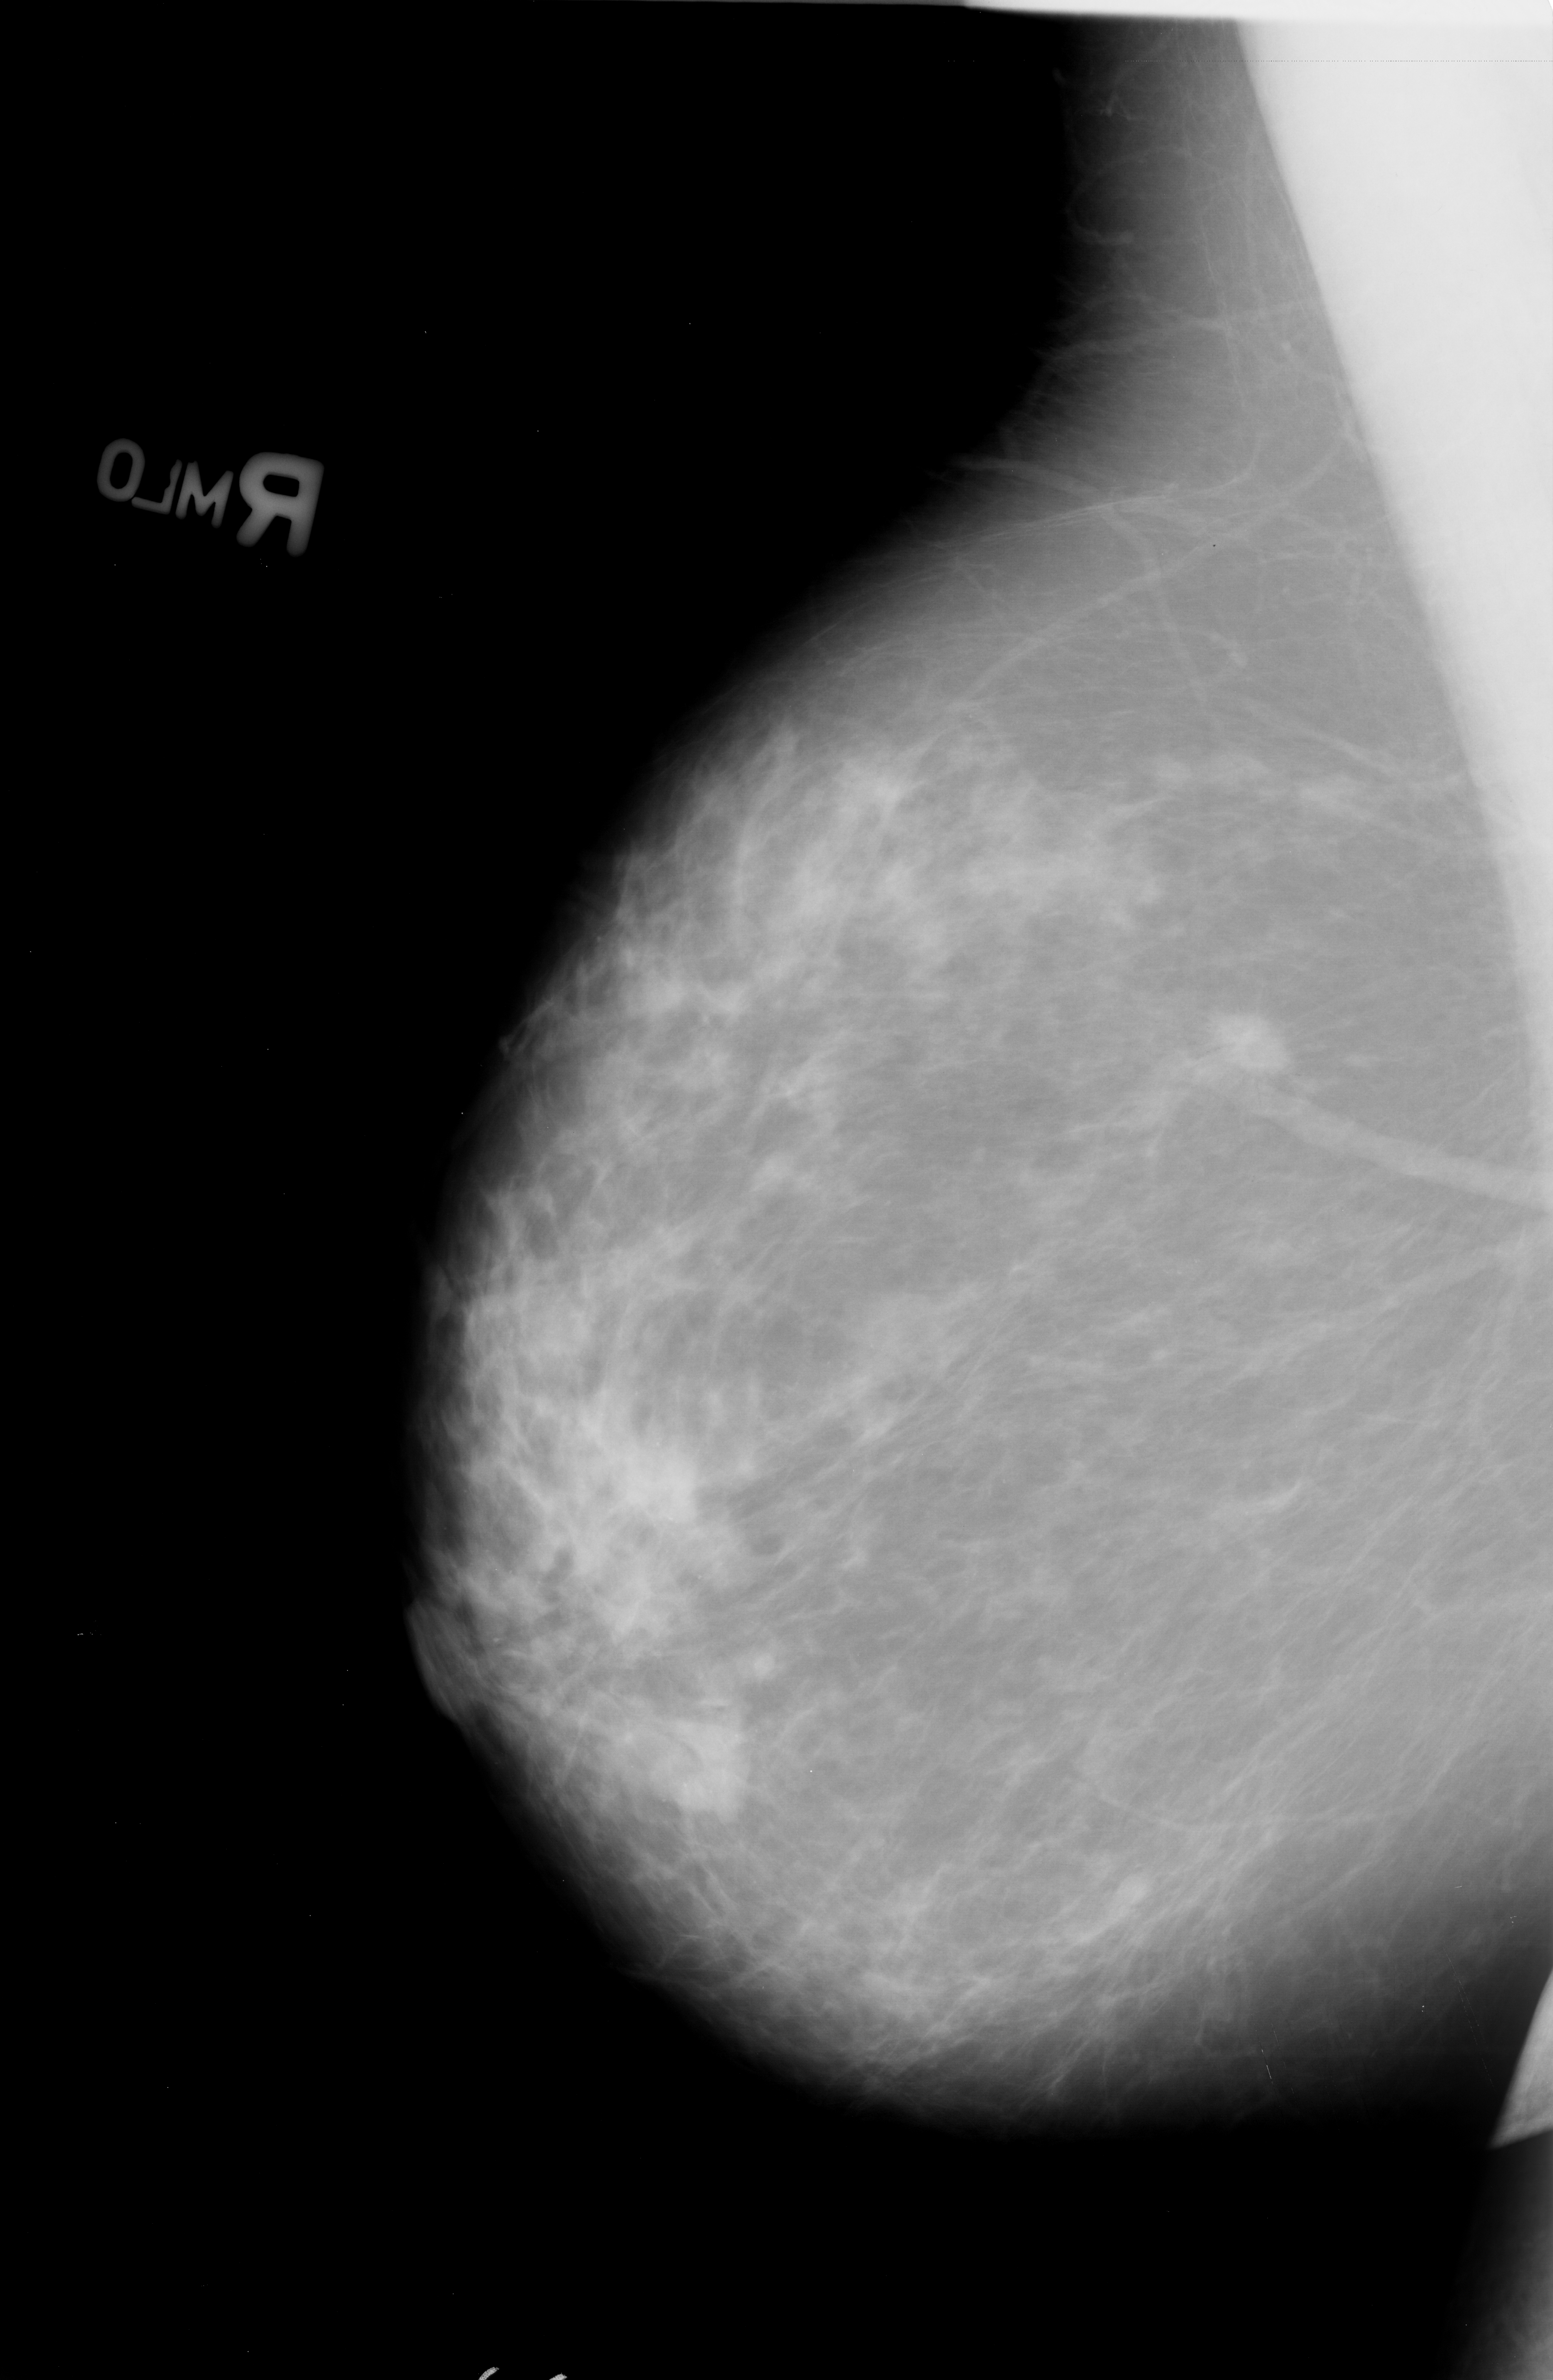
Digitized screen-film mammogram. Right breast. MLO view. Breast composition: scattered fibroglandular densities (BI-RADS density category 2 of 4). 1553 × 2380 image matrix.
Marked abnormalities (boxes around the expert regions of interest):
- mass, shape oval, margins spiculated; BI-RADS assessment category 5; subtlety rating 4 on a 1 (subtle) to 5 (obvious) scale; pathology result (as recorded, not read from the image): malignant: bounding box (x1, y1, x2, y2) in pixels: (1180, 989, 1309, 1097)